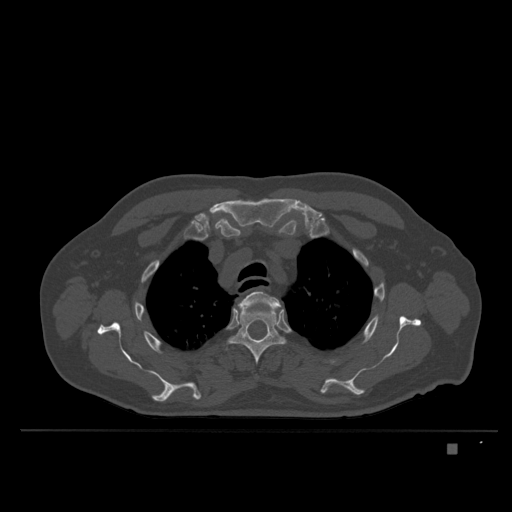
CT including the spine, one axial slice; position 290 of 435 along the scan axis; bone window (W 1800 / L 400 HU); 1.5 mm slice thickness; 512 × 512 image matrix, field of view 434 × 434 mm. Male patient, age 73 years. Case-level facts recorded for this patient, not image findings: primary cancer: skin.
Structures marked on this image (semi-automatically segmented with operator editing):
- T3 vertebra: box from (x=238, y=291) to (x=282, y=308) px
- T4 vertebra: (x=229, y=309)–(x=285, y=376)